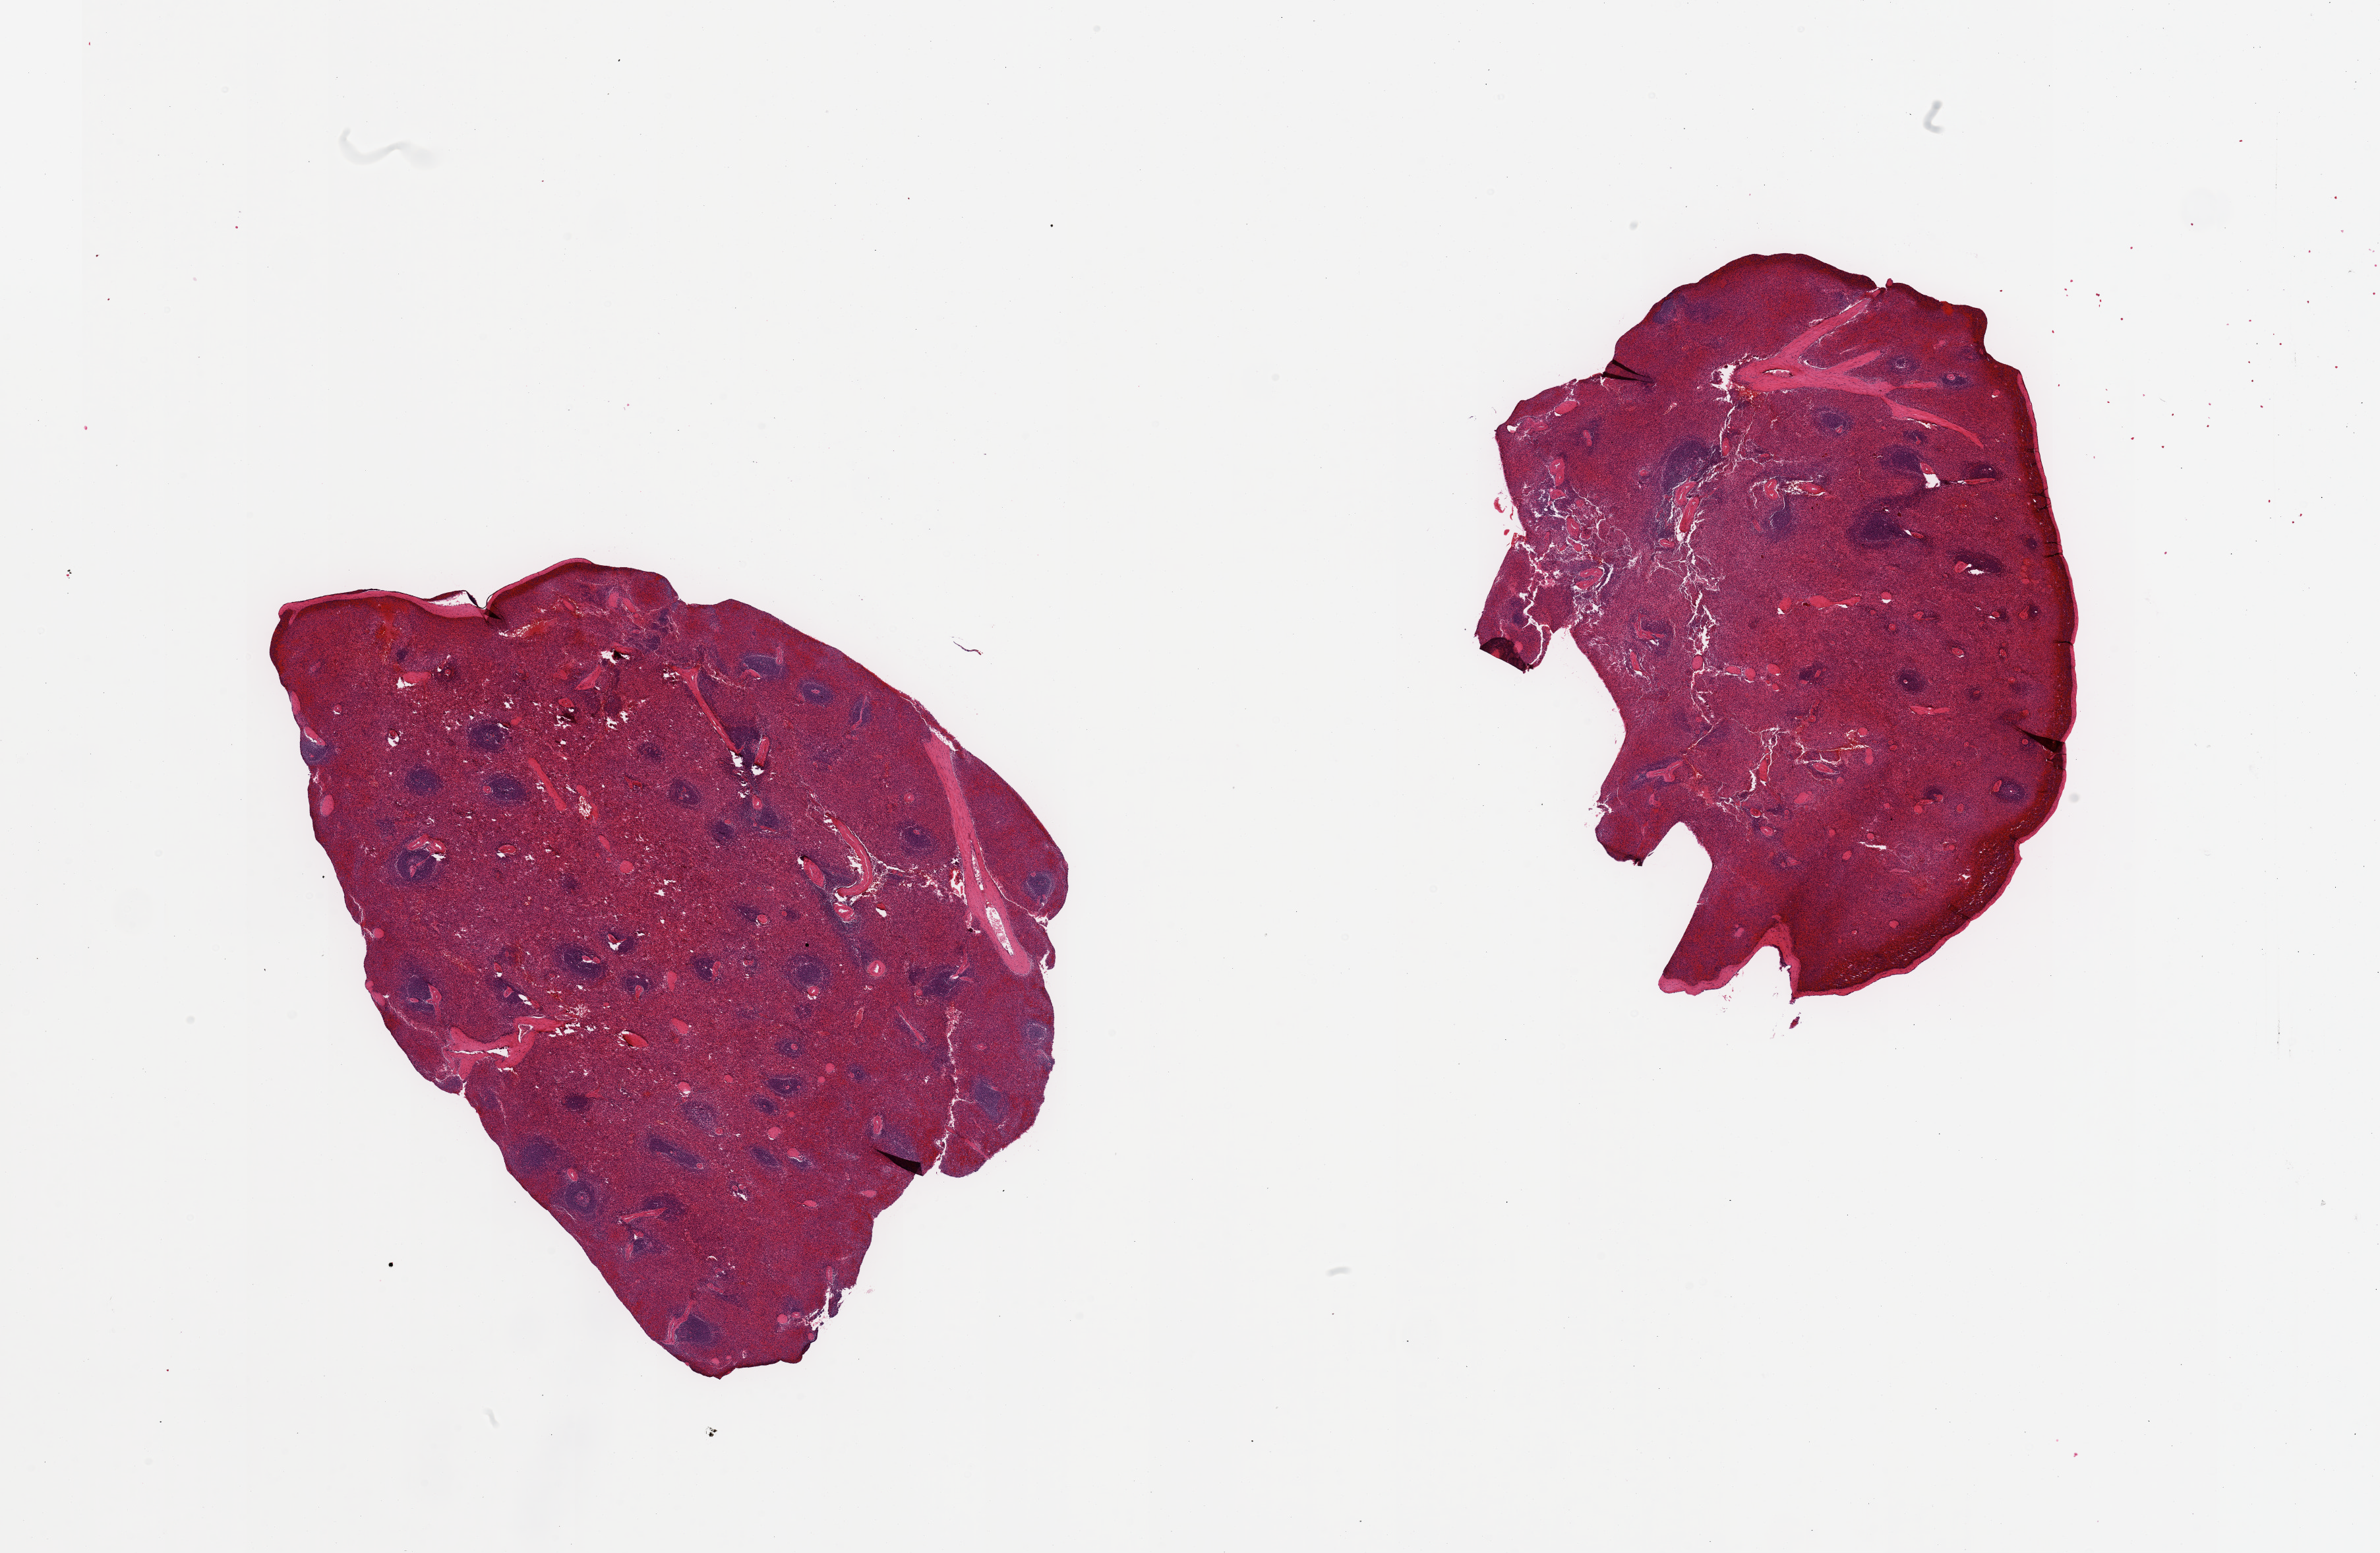
Digitized hematoxylin and eosin (H&E)-stained section, shown as a low-resolution overview of the whole scanned area (about 28.5 x 18.6 mm); PAXgene-fixed paraffin-embedded (PFPE) section; sampled site (target tissue): spleen; tissue donor sample.
- reviewer comment on this tissue sample: 2 pieces, no abnormalities